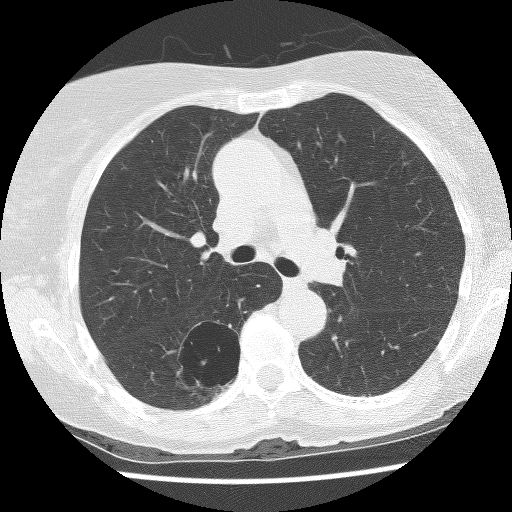
Low-dose screening chest CT, axial slice. First (baseline) screen. Lung window (W 1500 / L -600 HU). Female, age 69 years at enrolment. Former smoker at enrolment.
Expert-annotated lung lesion, bounding box <164,321,246,395> (left, top, right, bottom; pixels). The screening reader recorded 2 non-calcified nodules or masses ≥4 mm on this exam; which of them this box marks is not recorded. Lung cancer was diagnosed 288 days after this screen: non-small cell carcinoma, right lower lobe, poorly differentiated (G3), stage IB (AJCC 6th edition), 36 mm at pathology.